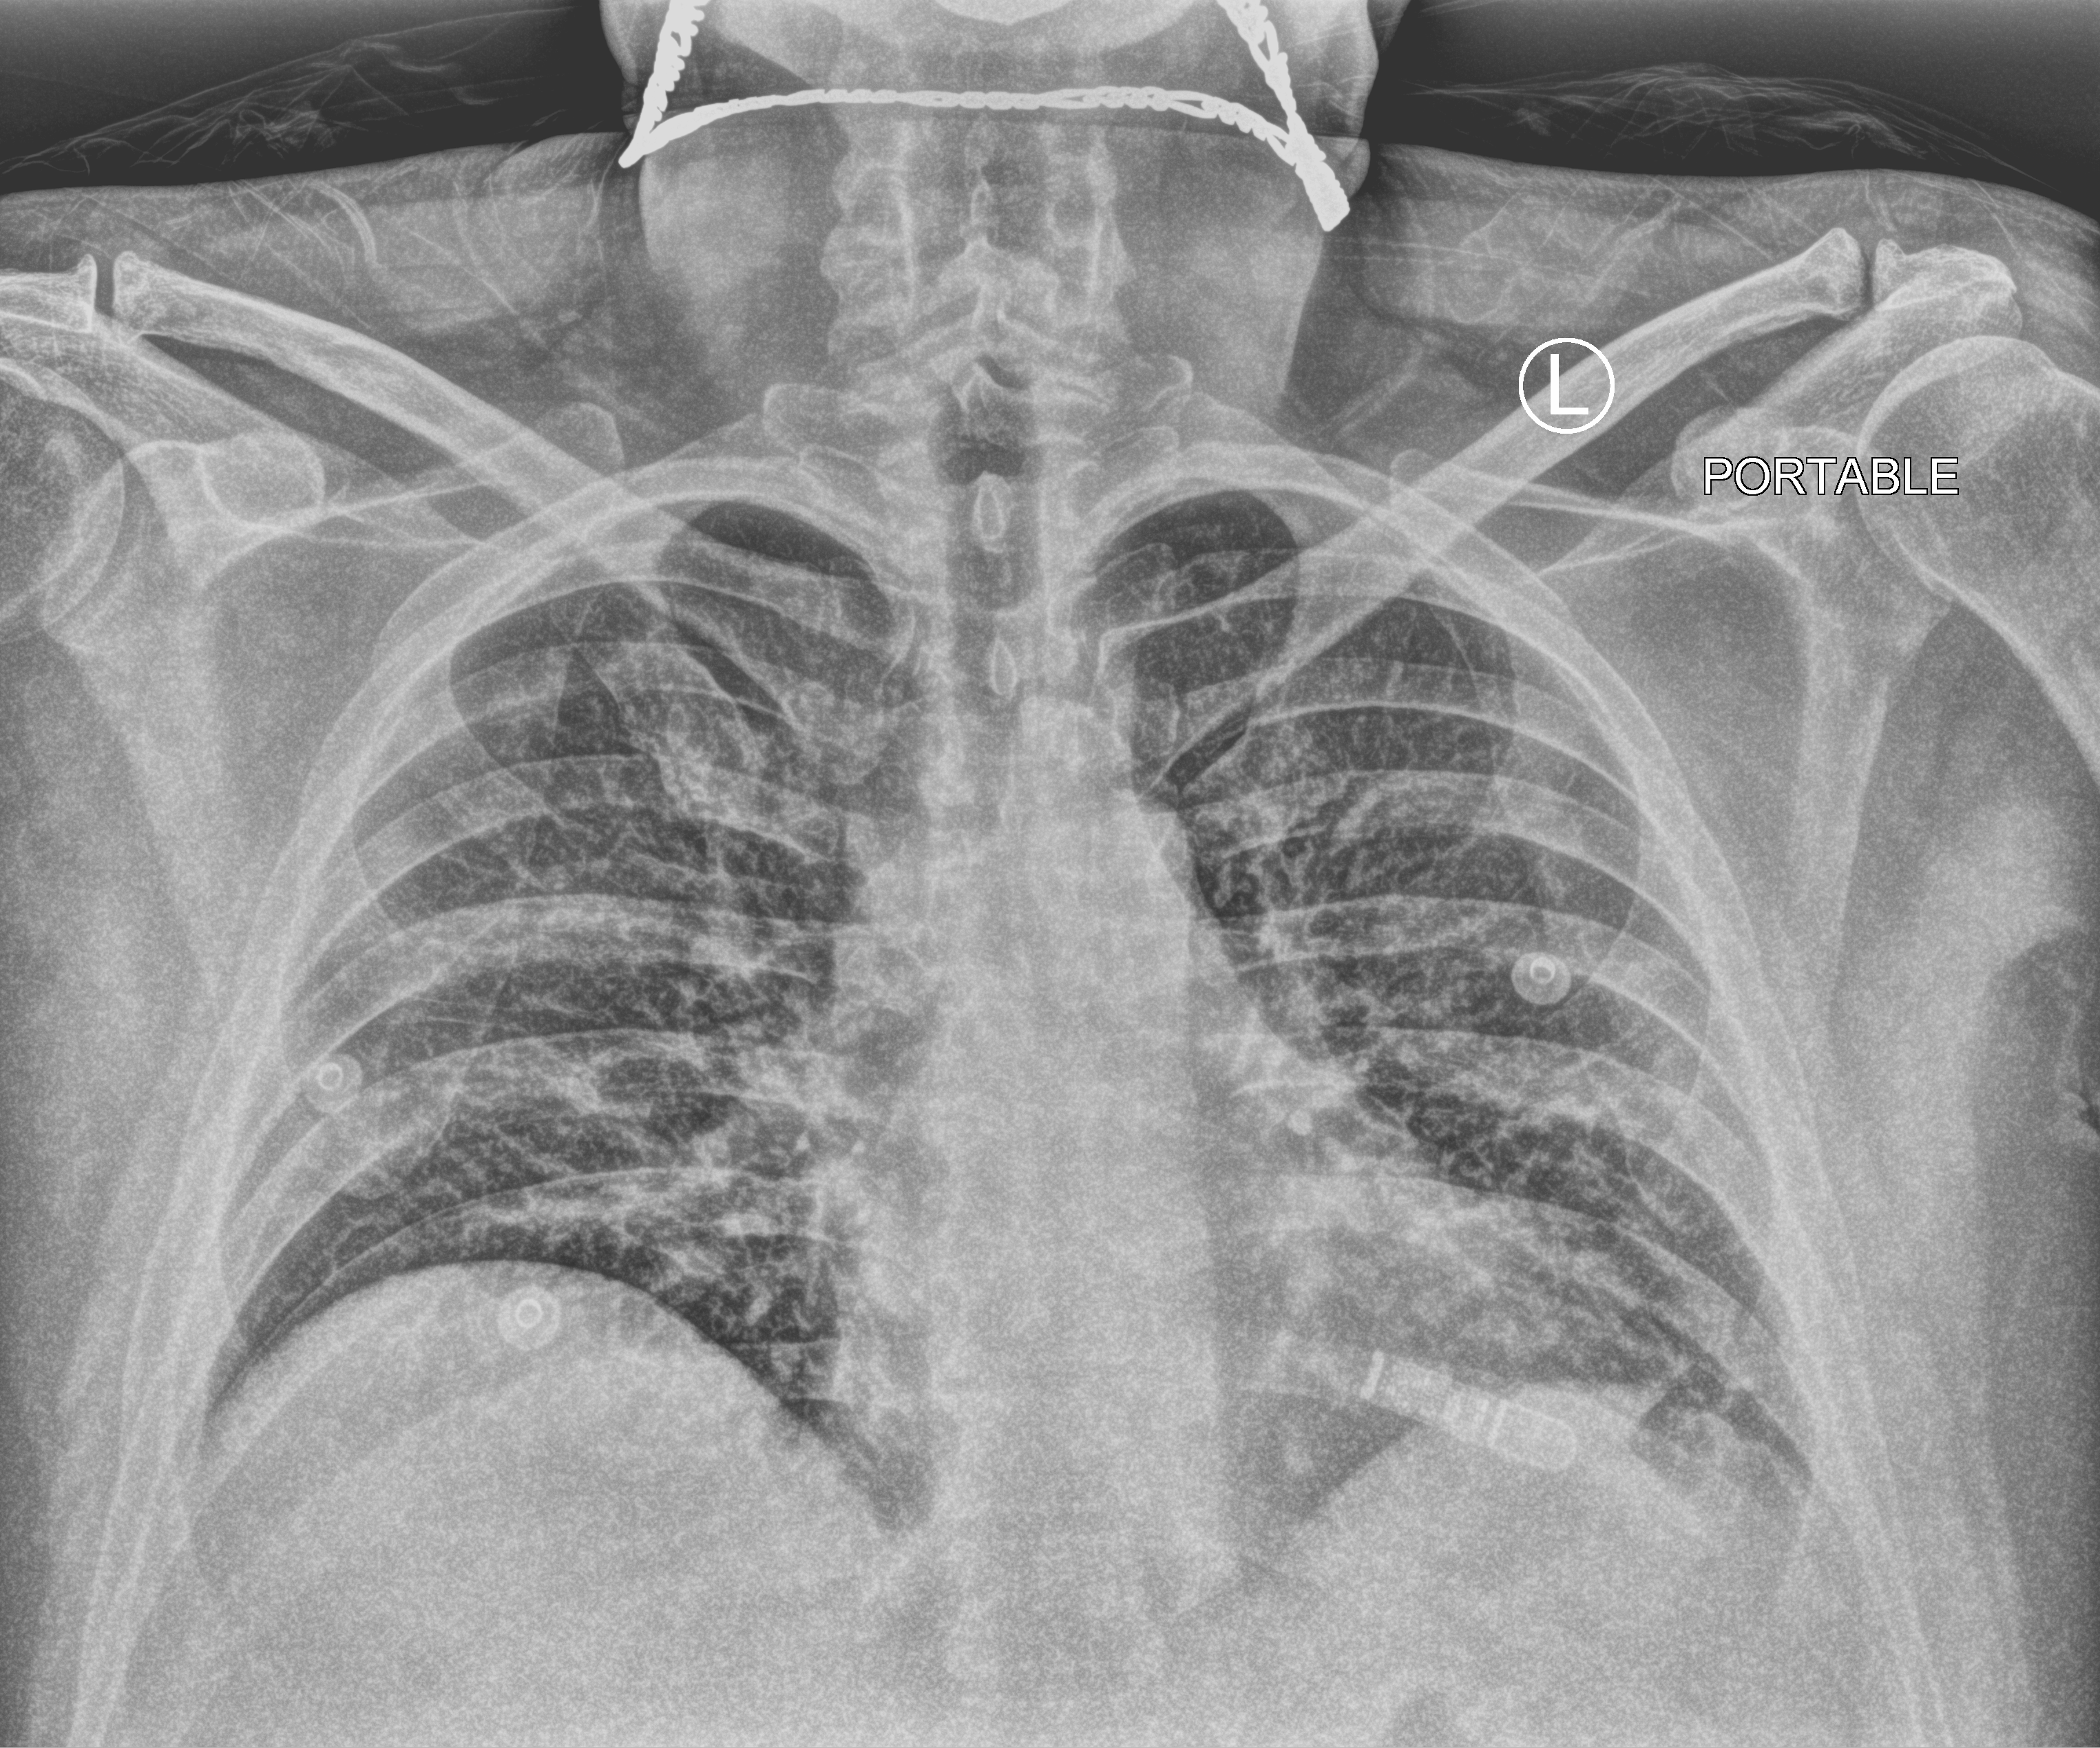
Chest X-ray (portable), anteroposterior (AP) projection. Male patient hospitalised with COVID-19, age 18–59 years.
Hospital-stay facts (about this admission, not read from this image; timing relative to this image not recorded): mechanically ventilated during this hospital stay: yes; admitted to intensive care during this hospital stay: yes.